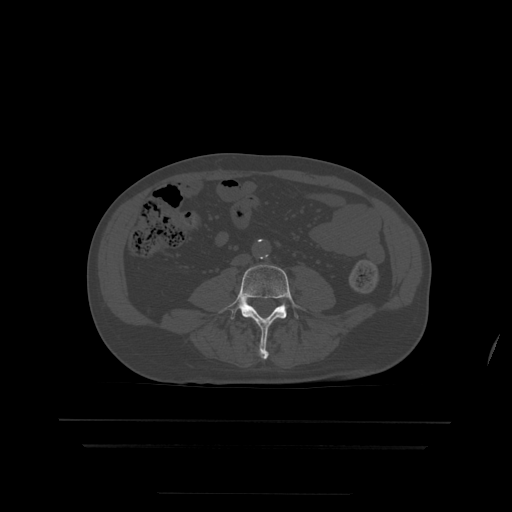
CT including the spine, one axial slice; position 95 of 522 along the scan axis; bone window (W 1800 / L 400 HU); 1.25 mm slice thickness; 512 × 512 image matrix, field of view 436 × 436 mm. Patient age 68 years. From the clinical record (not read from this slice): primary cancer: urothelial.
Structures marked on this image (semi-automatic segmentation, software-assisted and operator-edited):
- L4 vertebra: bounding box [x1, y1, x2, y2] px = [219, 264, 305, 360]